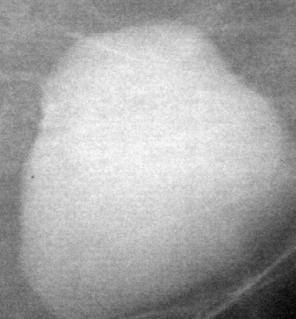
Region of interest cut from a scanned film mammogram (one marked finding), left breast, CC view.
Finding: mass, shape oval, margins circumscribed; BI-RADS assessment category 4; pathology (as recorded): benign.